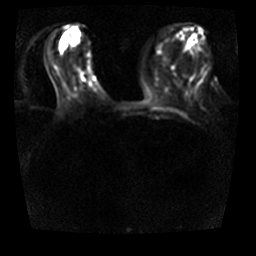
Breast MRI, one axial slice. Position 13 of 32 along the scan axis. Diffusion-weighted series; image 2 of 4 stored at this slice position (different b-values; order by instance number). 3 T. 256 × 256 image matrix, field of view 360 × 360 mm. Female patient.
Outlined on this slice (outlined manually by an expert reader):
- tumour on diffusion-weighted imaging: bounding box (x1, y1, x2, y2) in pixels: (79, 70, 81, 73)